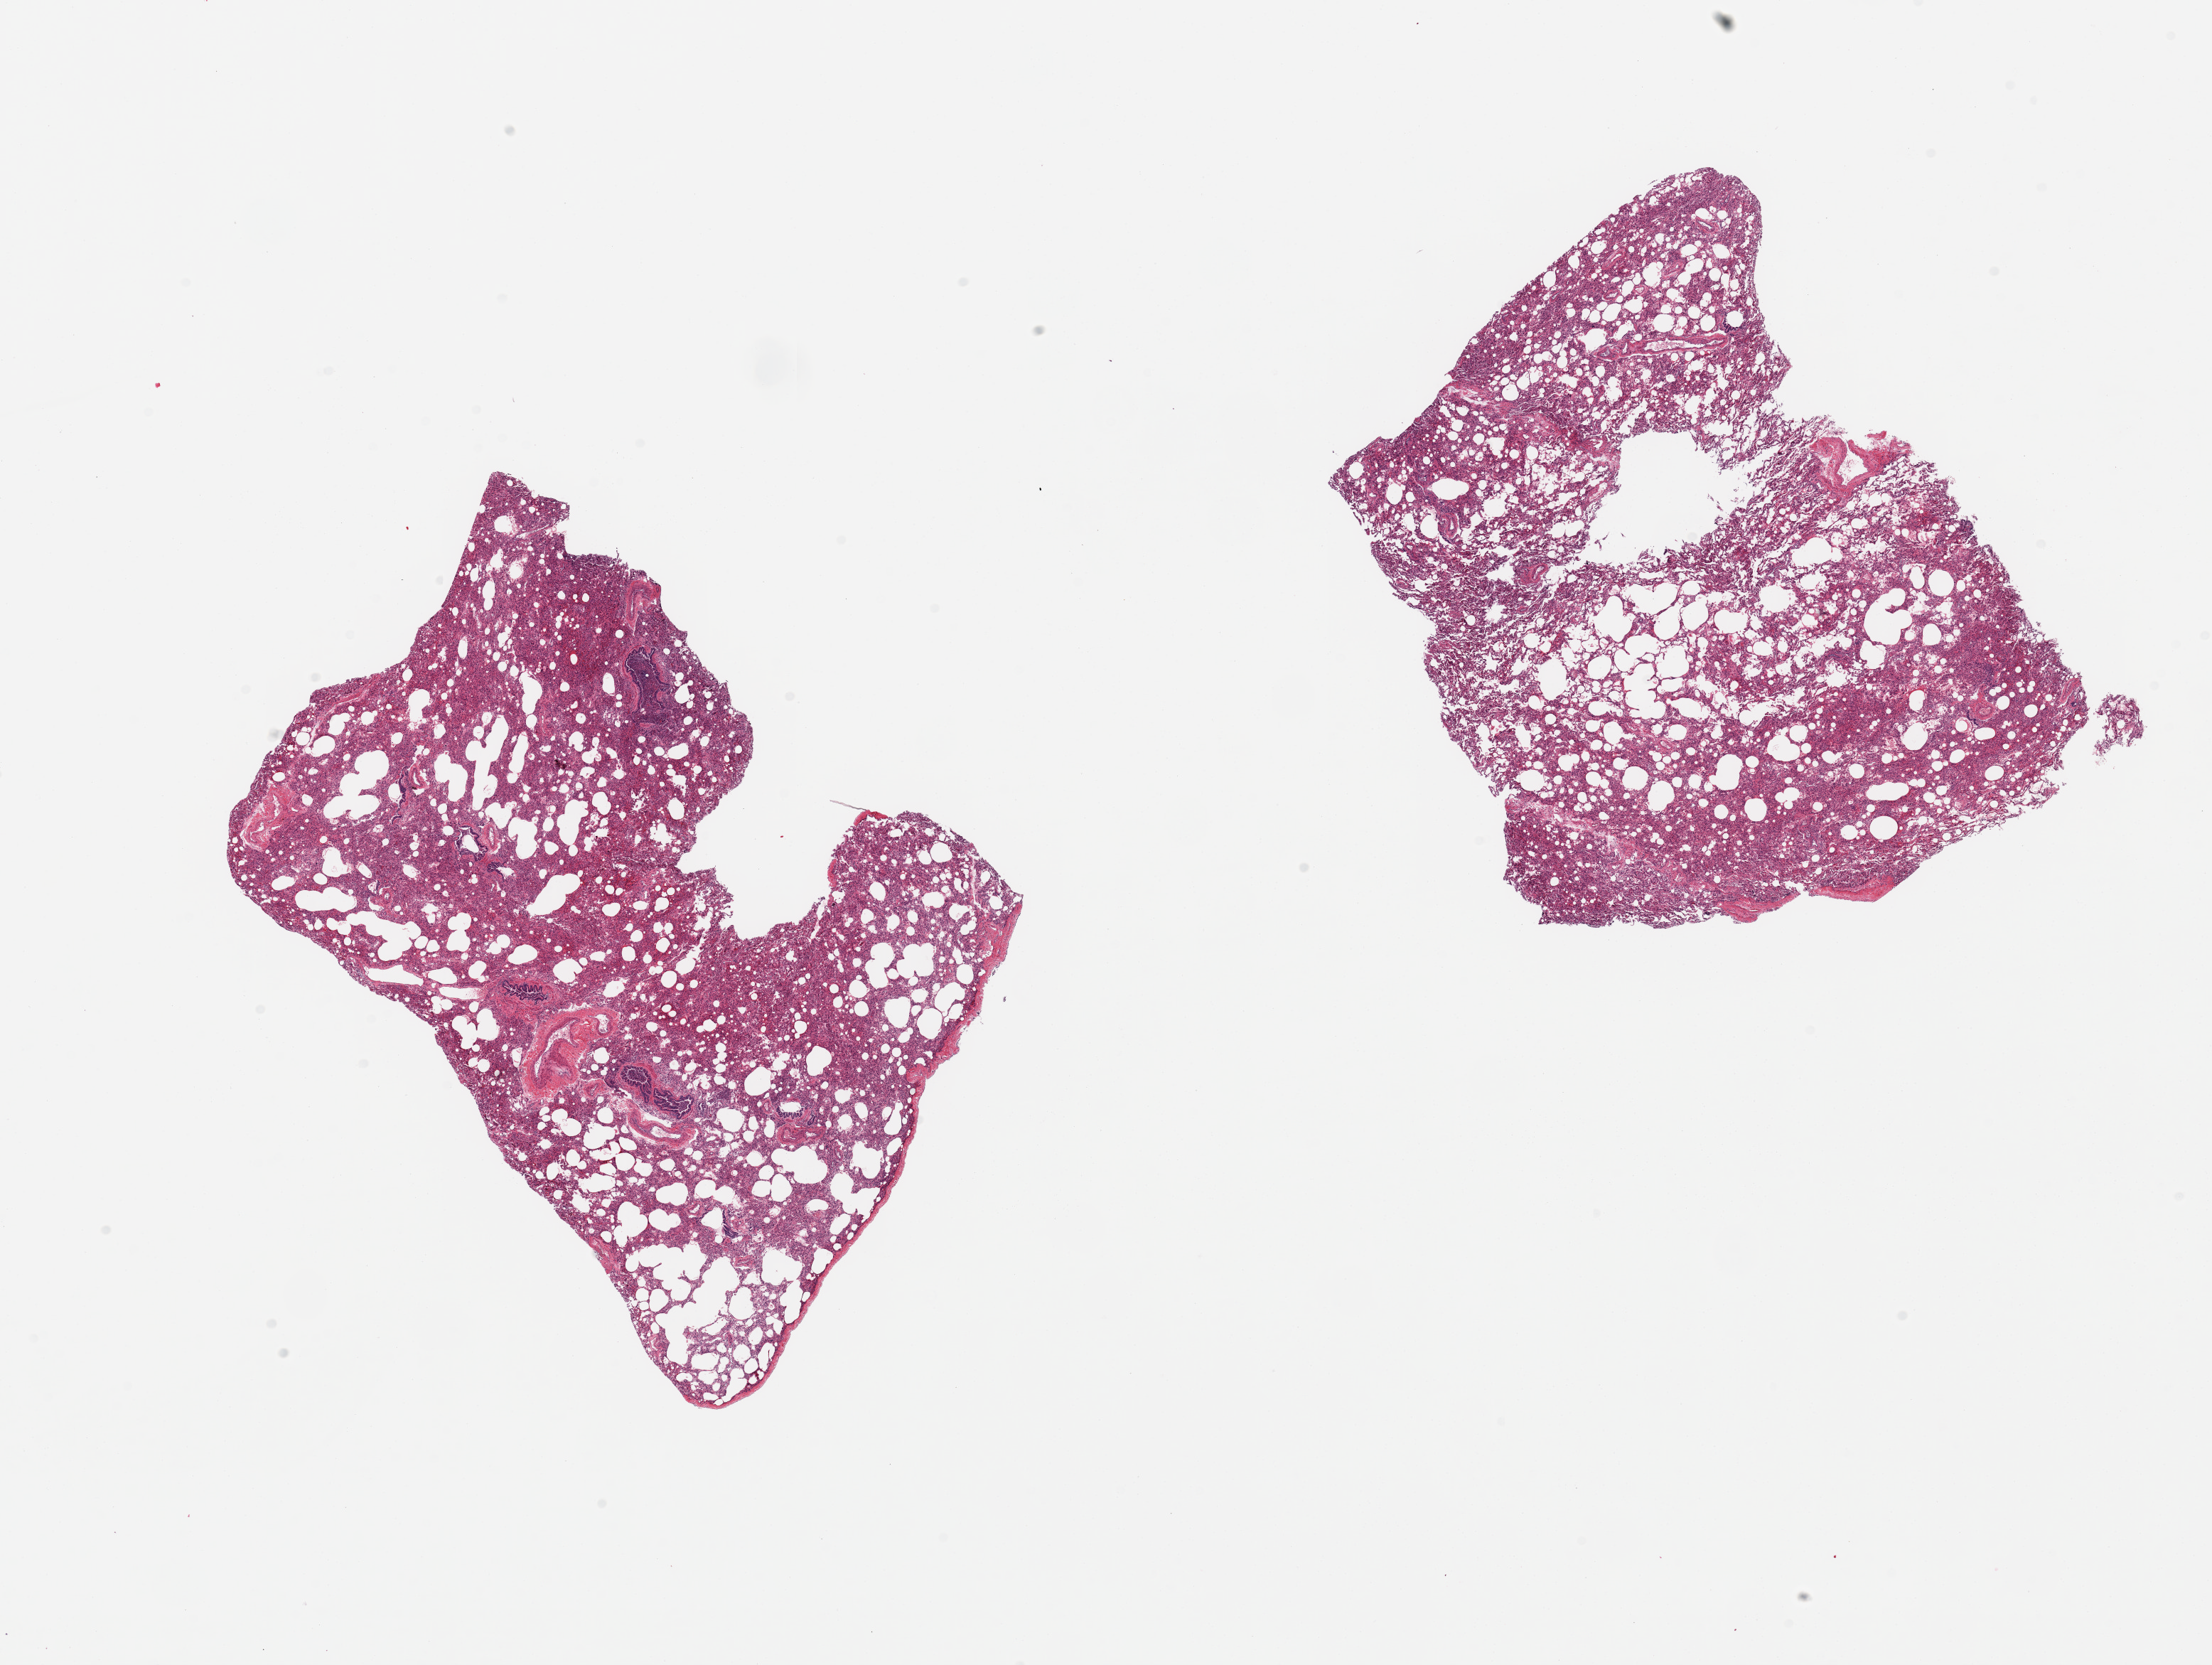
H&E whole-slide image, low-resolution overview of the scanned area, about 24.6 x 18.5 mm (acquisition: 20x scan). PAXgene-fixed paraffin-embedded (PFPE) section. Target tissue: lung. Tissue donor sample. Female donor.
- pathologist's review note for this sample: 2 pieces; bronchopneumonia 30%